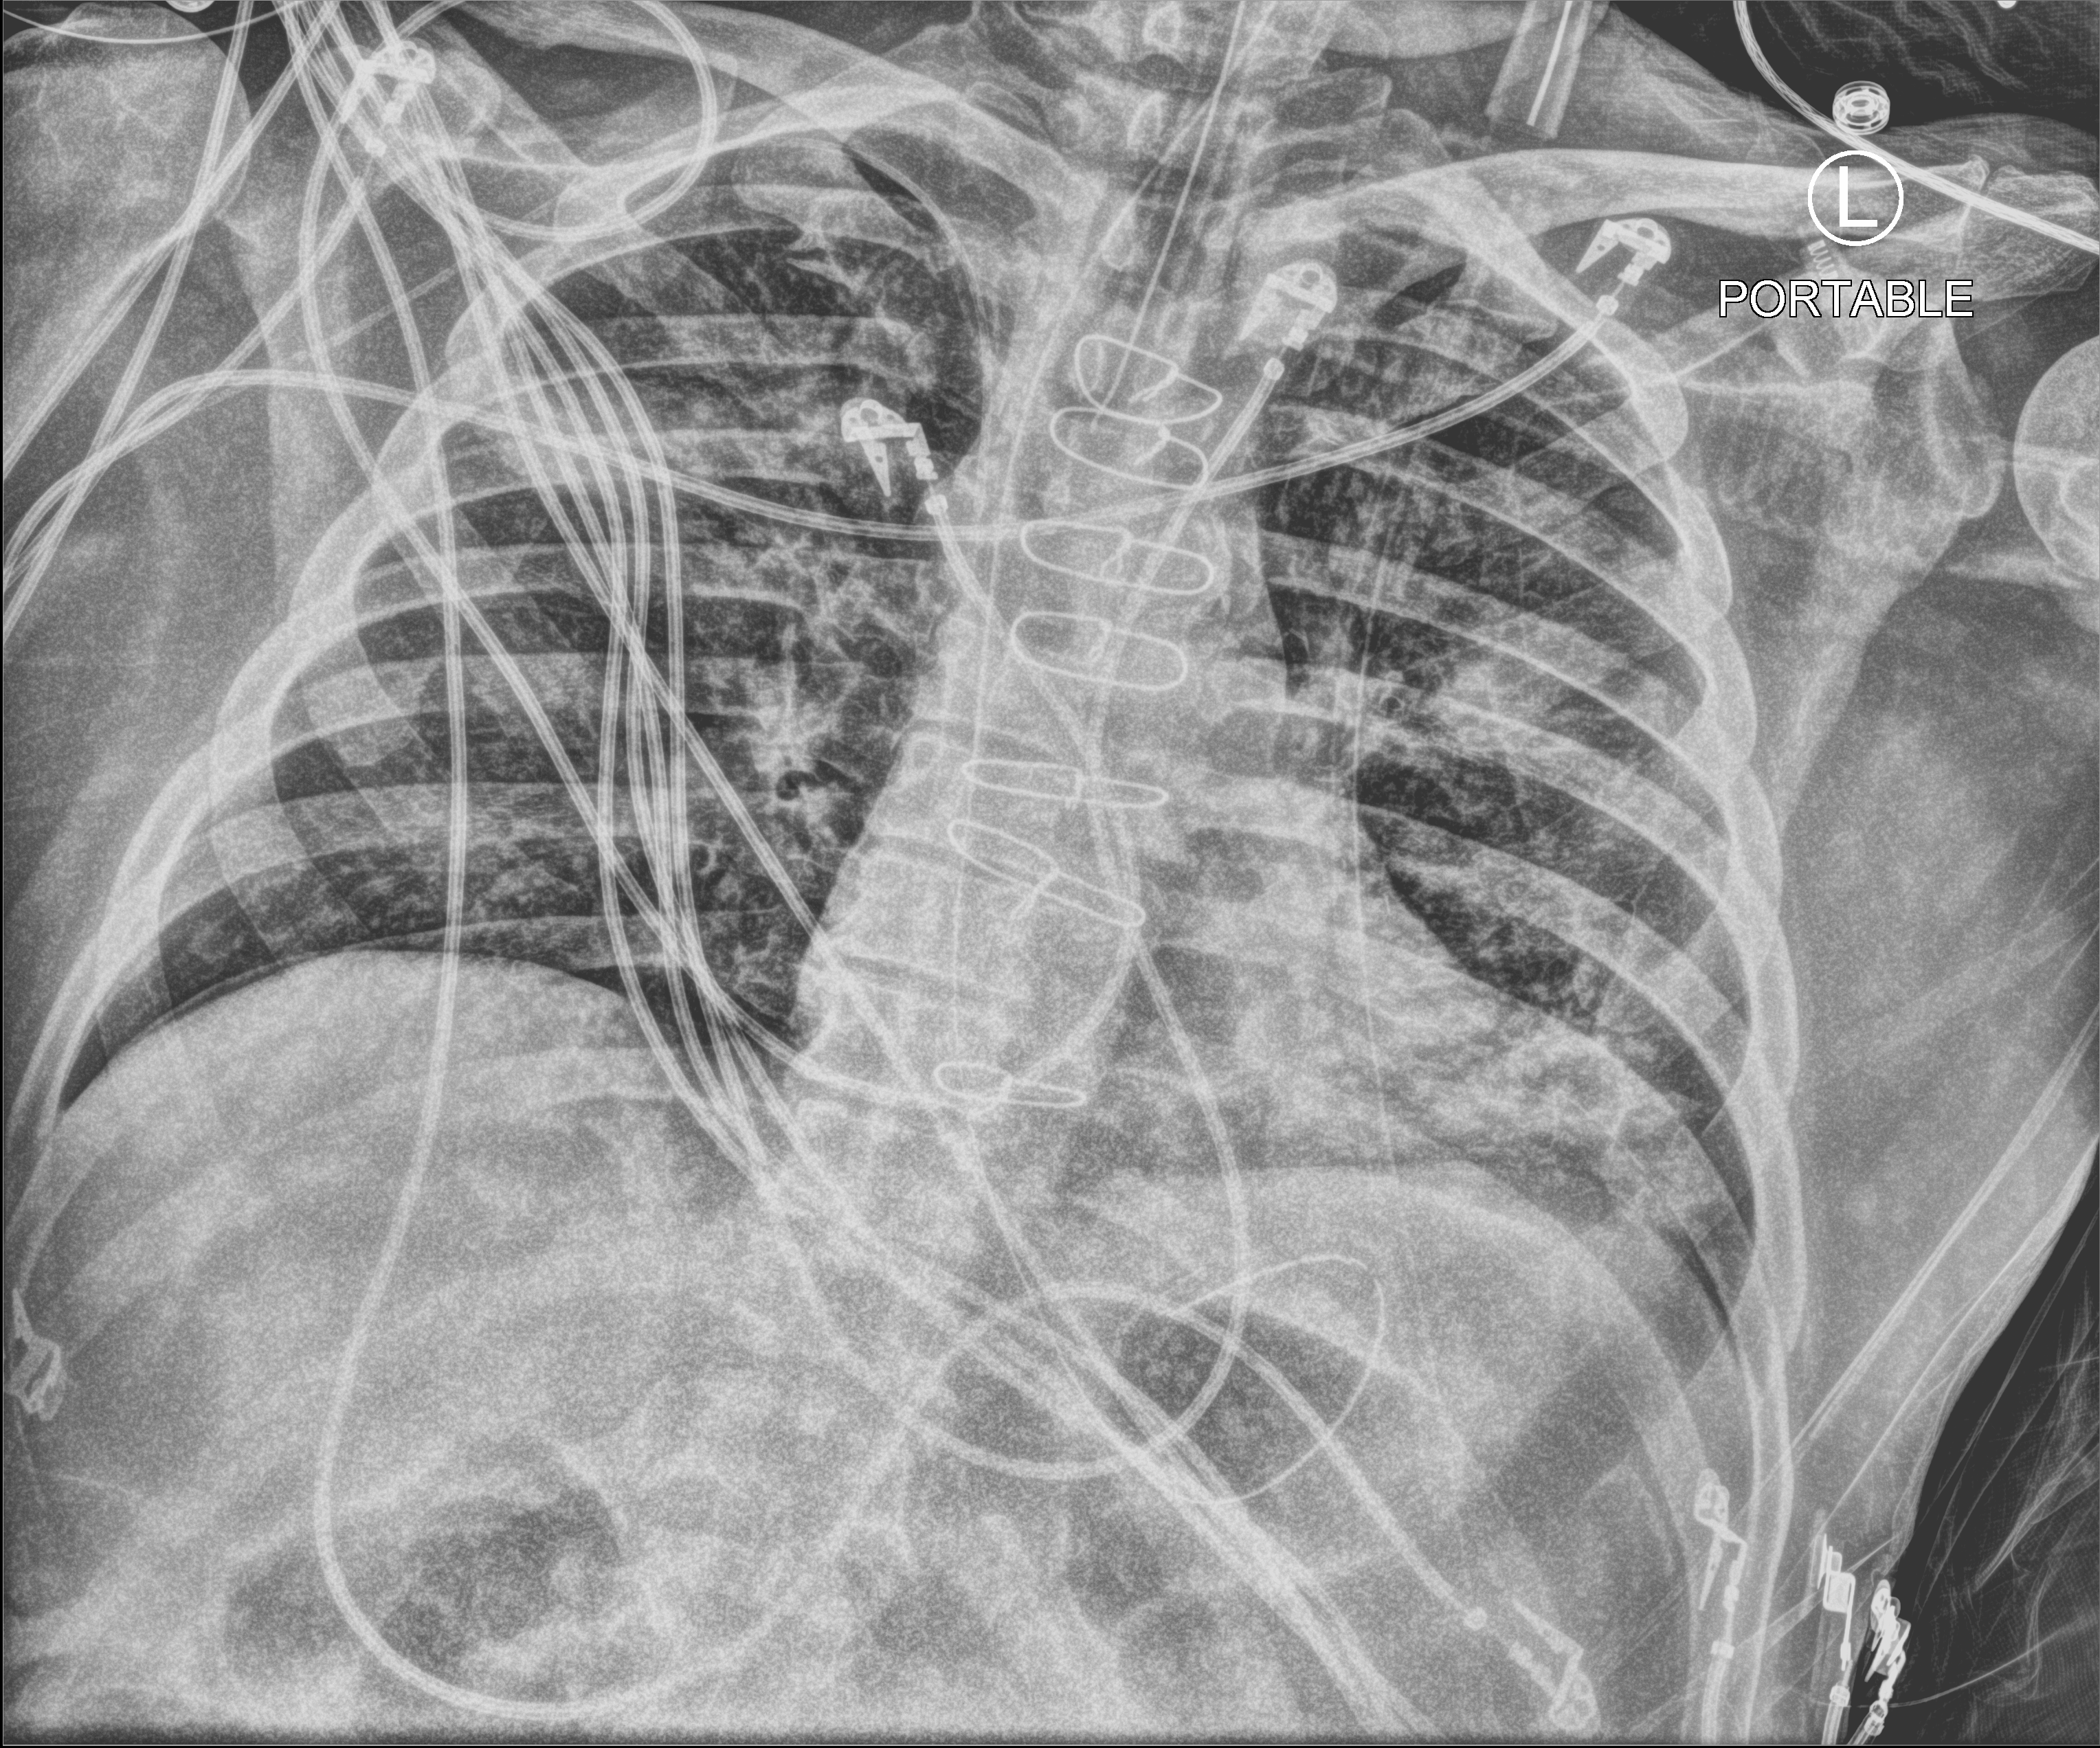
Portable chest radiograph, anteroposterior (AP) projection. Male patient hospitalised with COVID-19, age 60–74 years.
From the hospital-stay record, not from the radiograph (when in the stay this image was taken is not recorded):
- other chronic lung disease (admission record): no